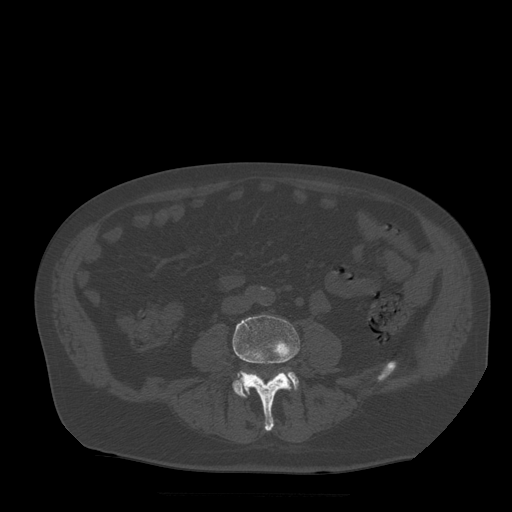
CT including the spine, one axial slice; slice 111 of 522 in the series (ordered by position); bone window (W 1800 / L 400 HU); 512 × 512 image matrix, field of view 420 × 420 mm. Patient age 72 years. Case-level facts recorded for this patient, not image findings: primary cancer: prostate.
Annotated regions visible in this slice (semi-automatic segmentation, software-assisted and operator-edited):
- L4 vertebra: bounding box (x1, y1, x2, y2) in pixels: (233, 315, 300, 432)
- L5 vertebra: (233, 372, 299, 398)